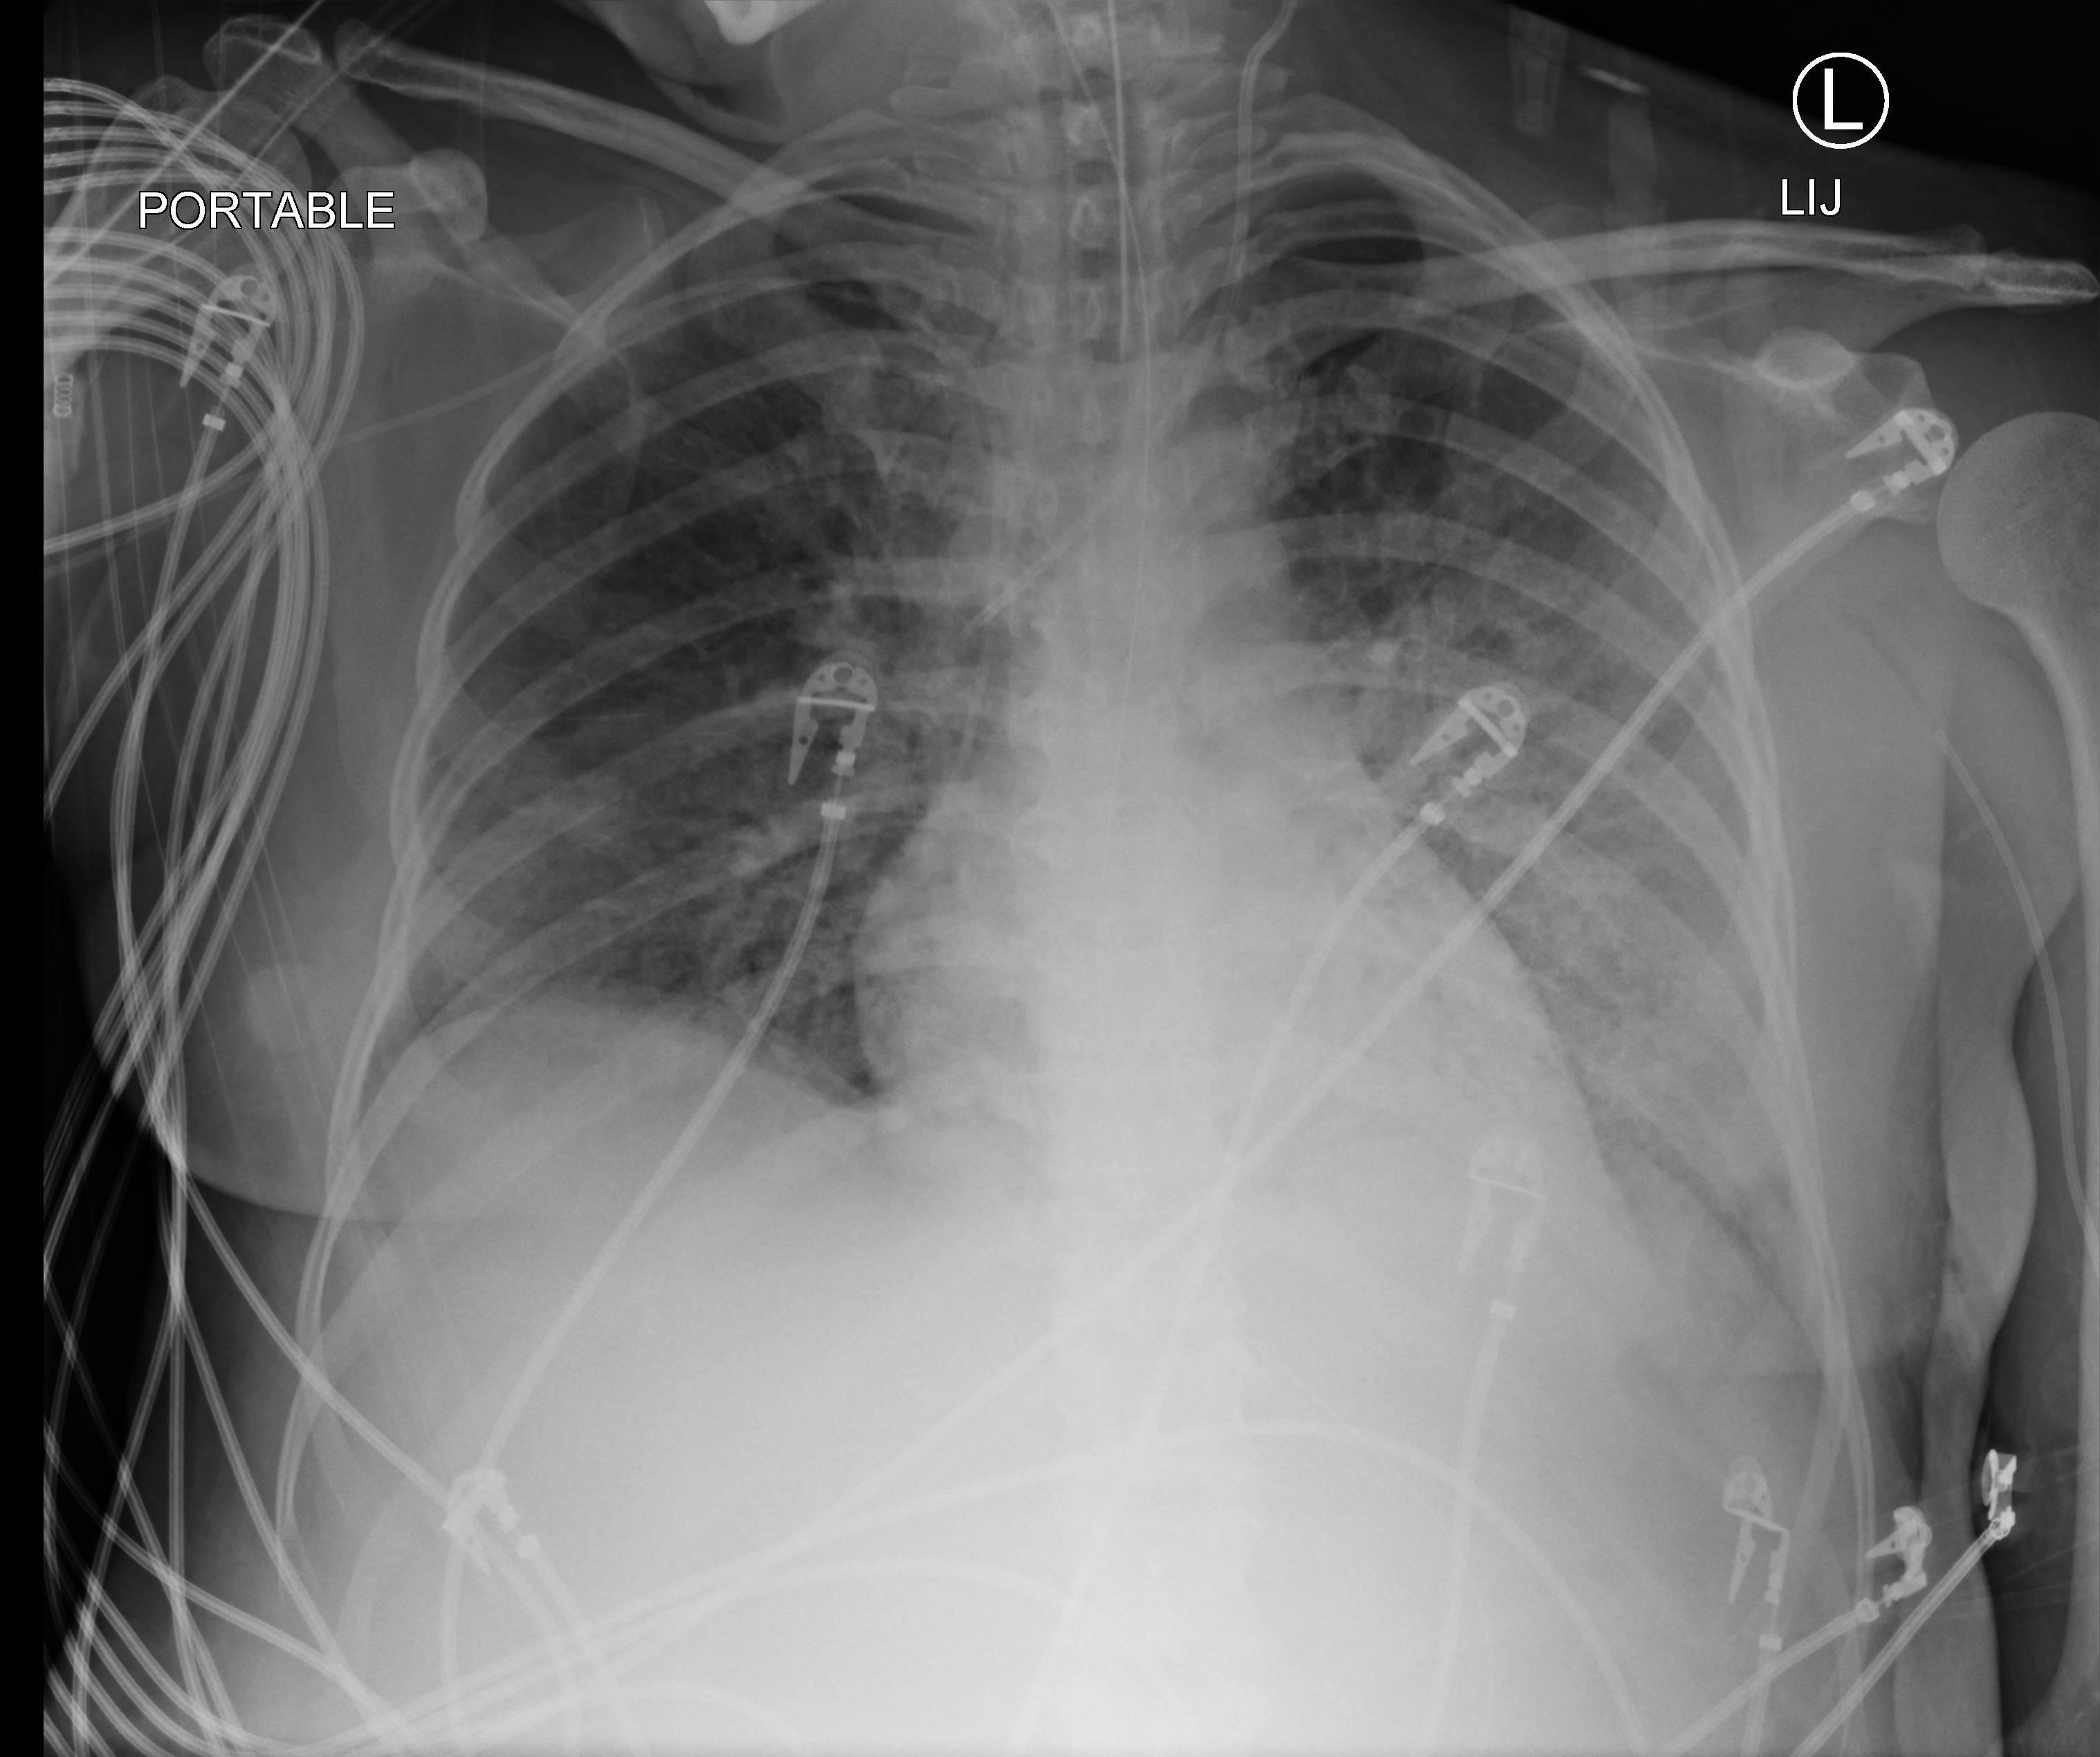
Portable chest radiograph, anteroposterior (AP) projection. Patient hospitalised with COVID-19; female, aged 18–59 years.
Hospital-stay facts (about this admission, not read from this image; timing relative to this image not recorded): mechanically ventilated during this hospital stay: yes.